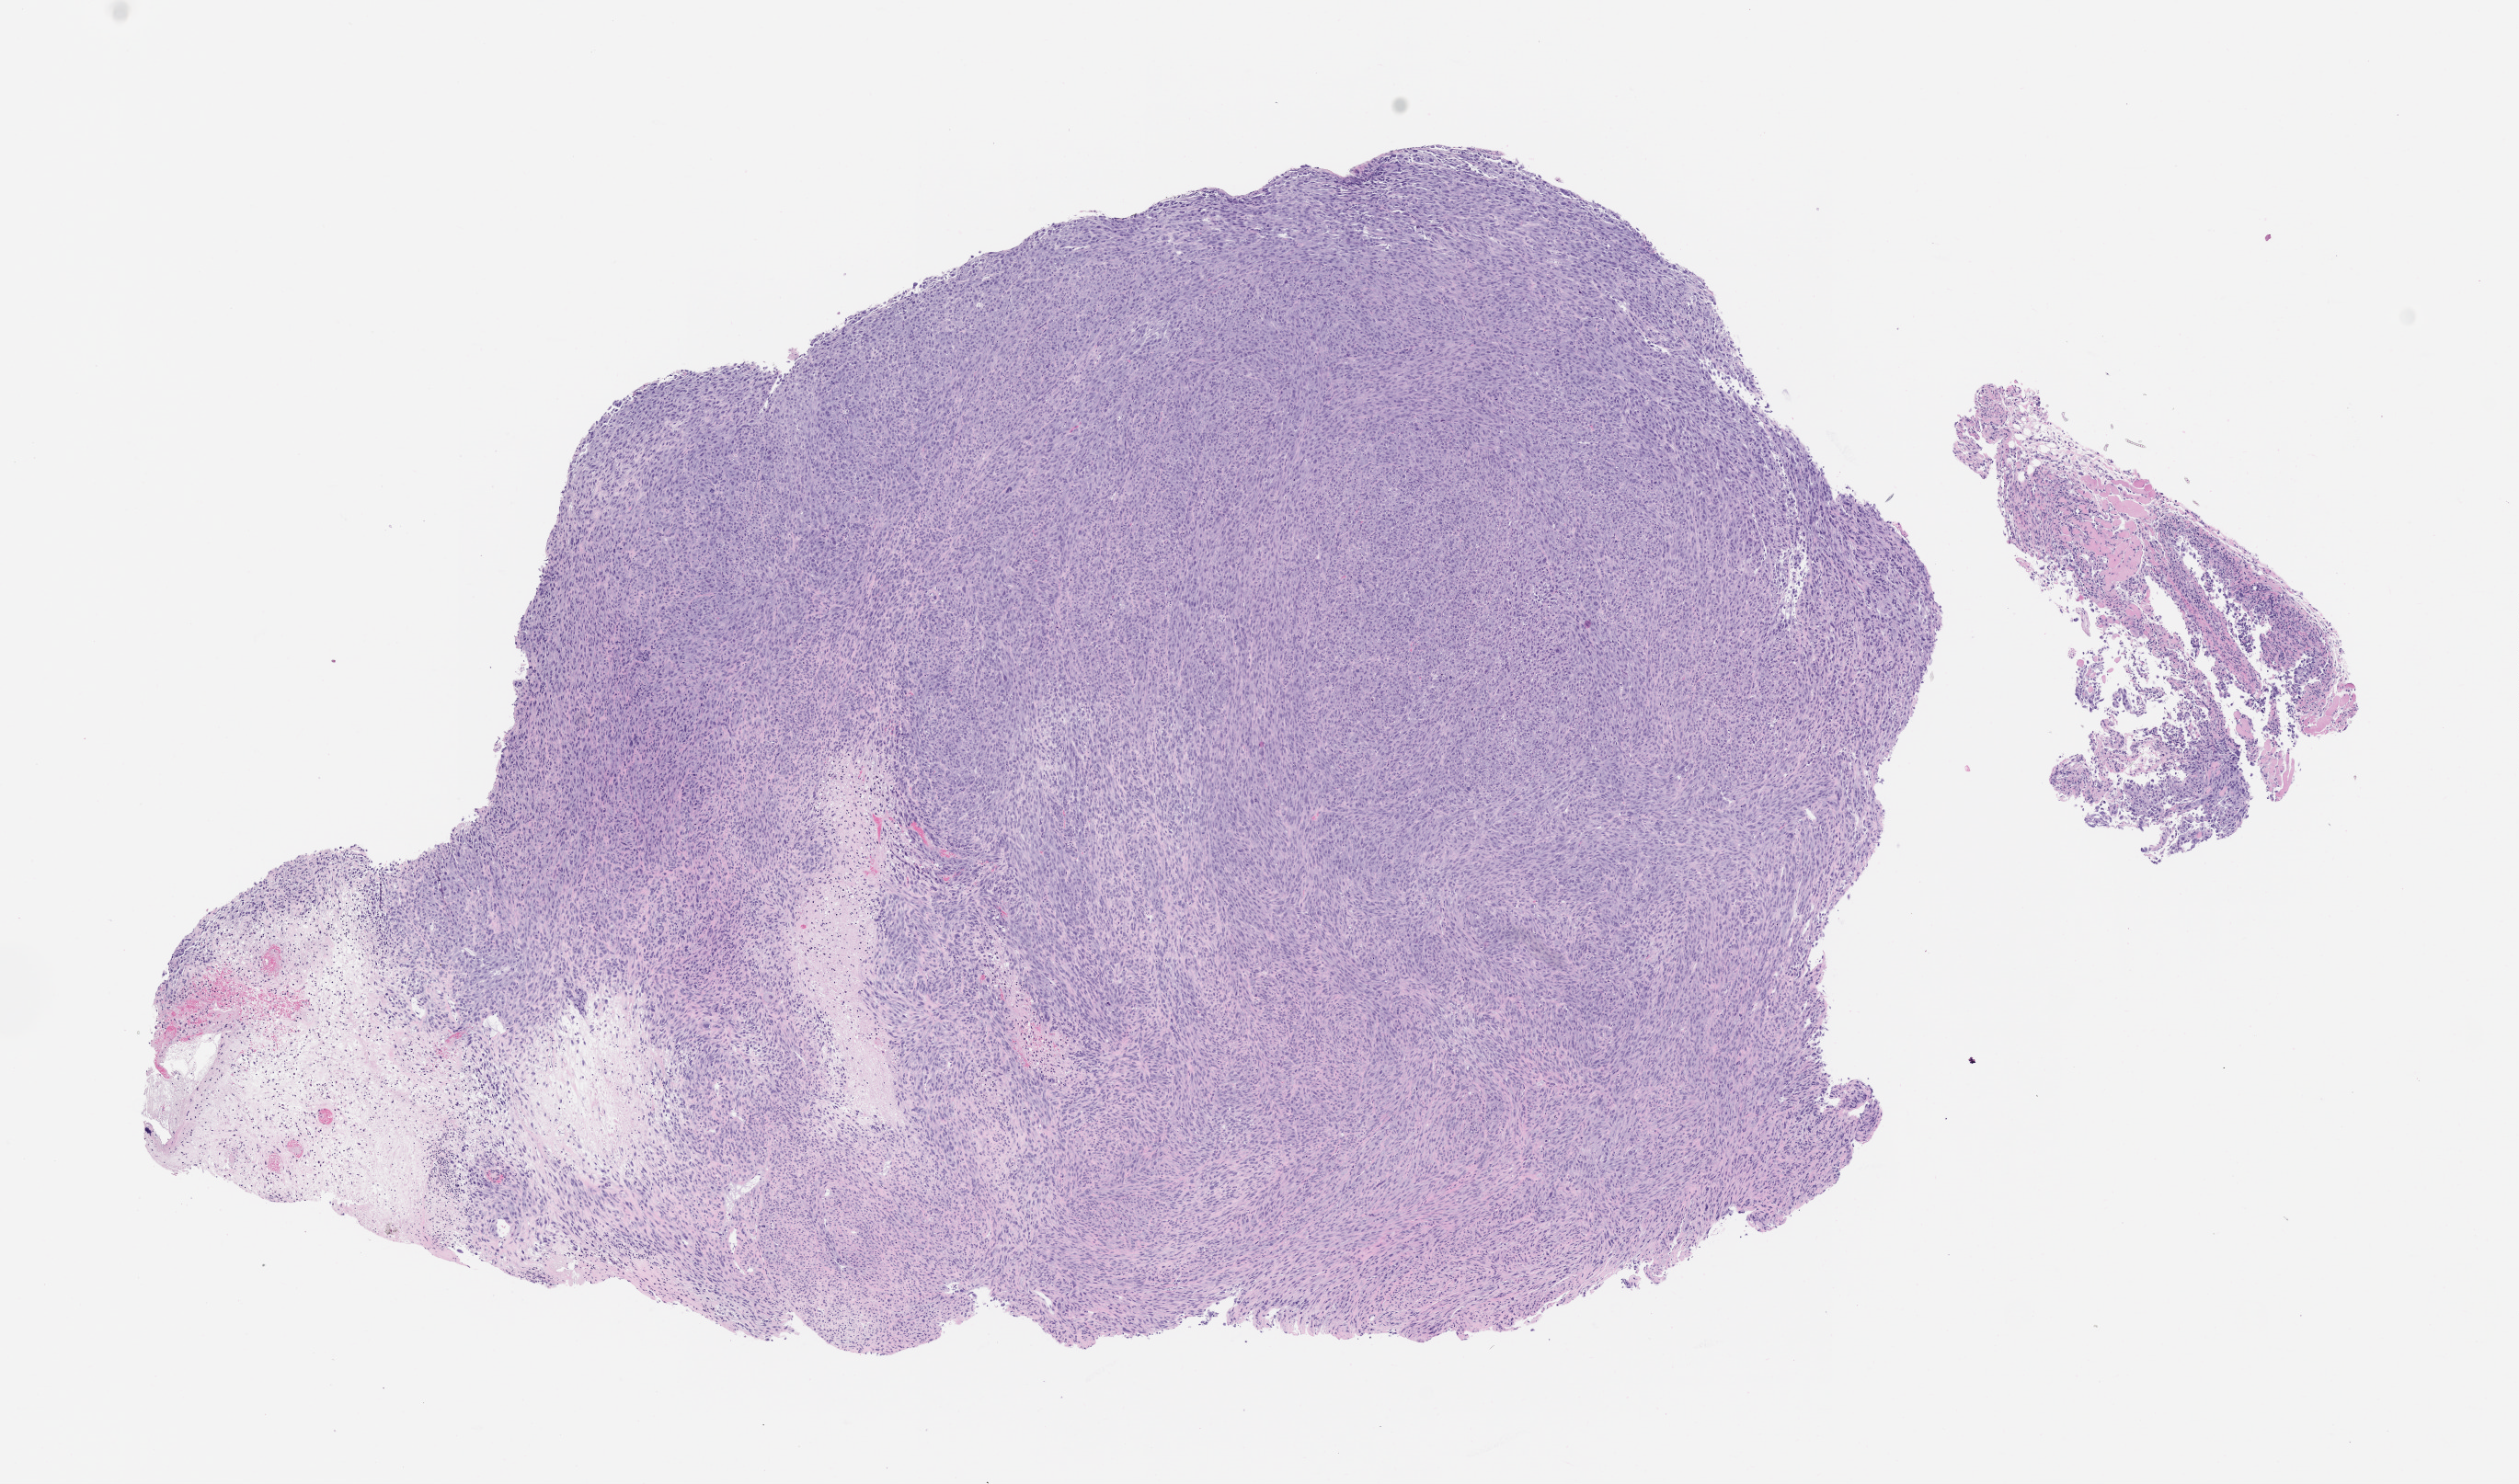
Haematoxylin and eosin whole-slide image of a patient-derived xenograft (PDX) tumor grown in a mouse, passage 2, whole scanned area (about 11.0 x 6.5 mm) shown as a low-resolution overview. Formalin-fixed paraffin-embedded section. Originating tumor site category: bone.
- originating patient diagnosis: Osteosarcoma